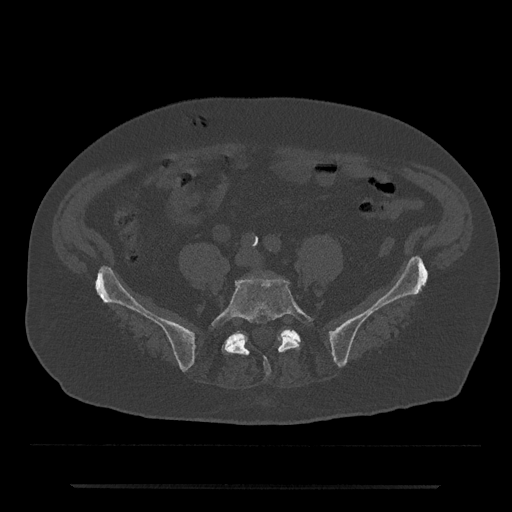
CT including the spine, one axial slice; position 281 of 797 along the scan axis; reconstruction kernel Br40s/3; 120 kVp; bone window (W 1800 / L 400 HU); 0.5 mm slice thickness; 512 × 512 image matrix, field of view 434 × 434 mm. Male patient, age 80 years. Case-level facts recorded for this patient, not image findings: primary cancer: prostate; vertebrae with lytic lesions (as recorded): L1, T11.
Annotated regions visible in this slice (semi-automatic segmentation, software-assisted and operator-edited):
- L5 vertebra: bounding box (x1, y1, x2, y2) in pixels: (211, 276, 313, 376)